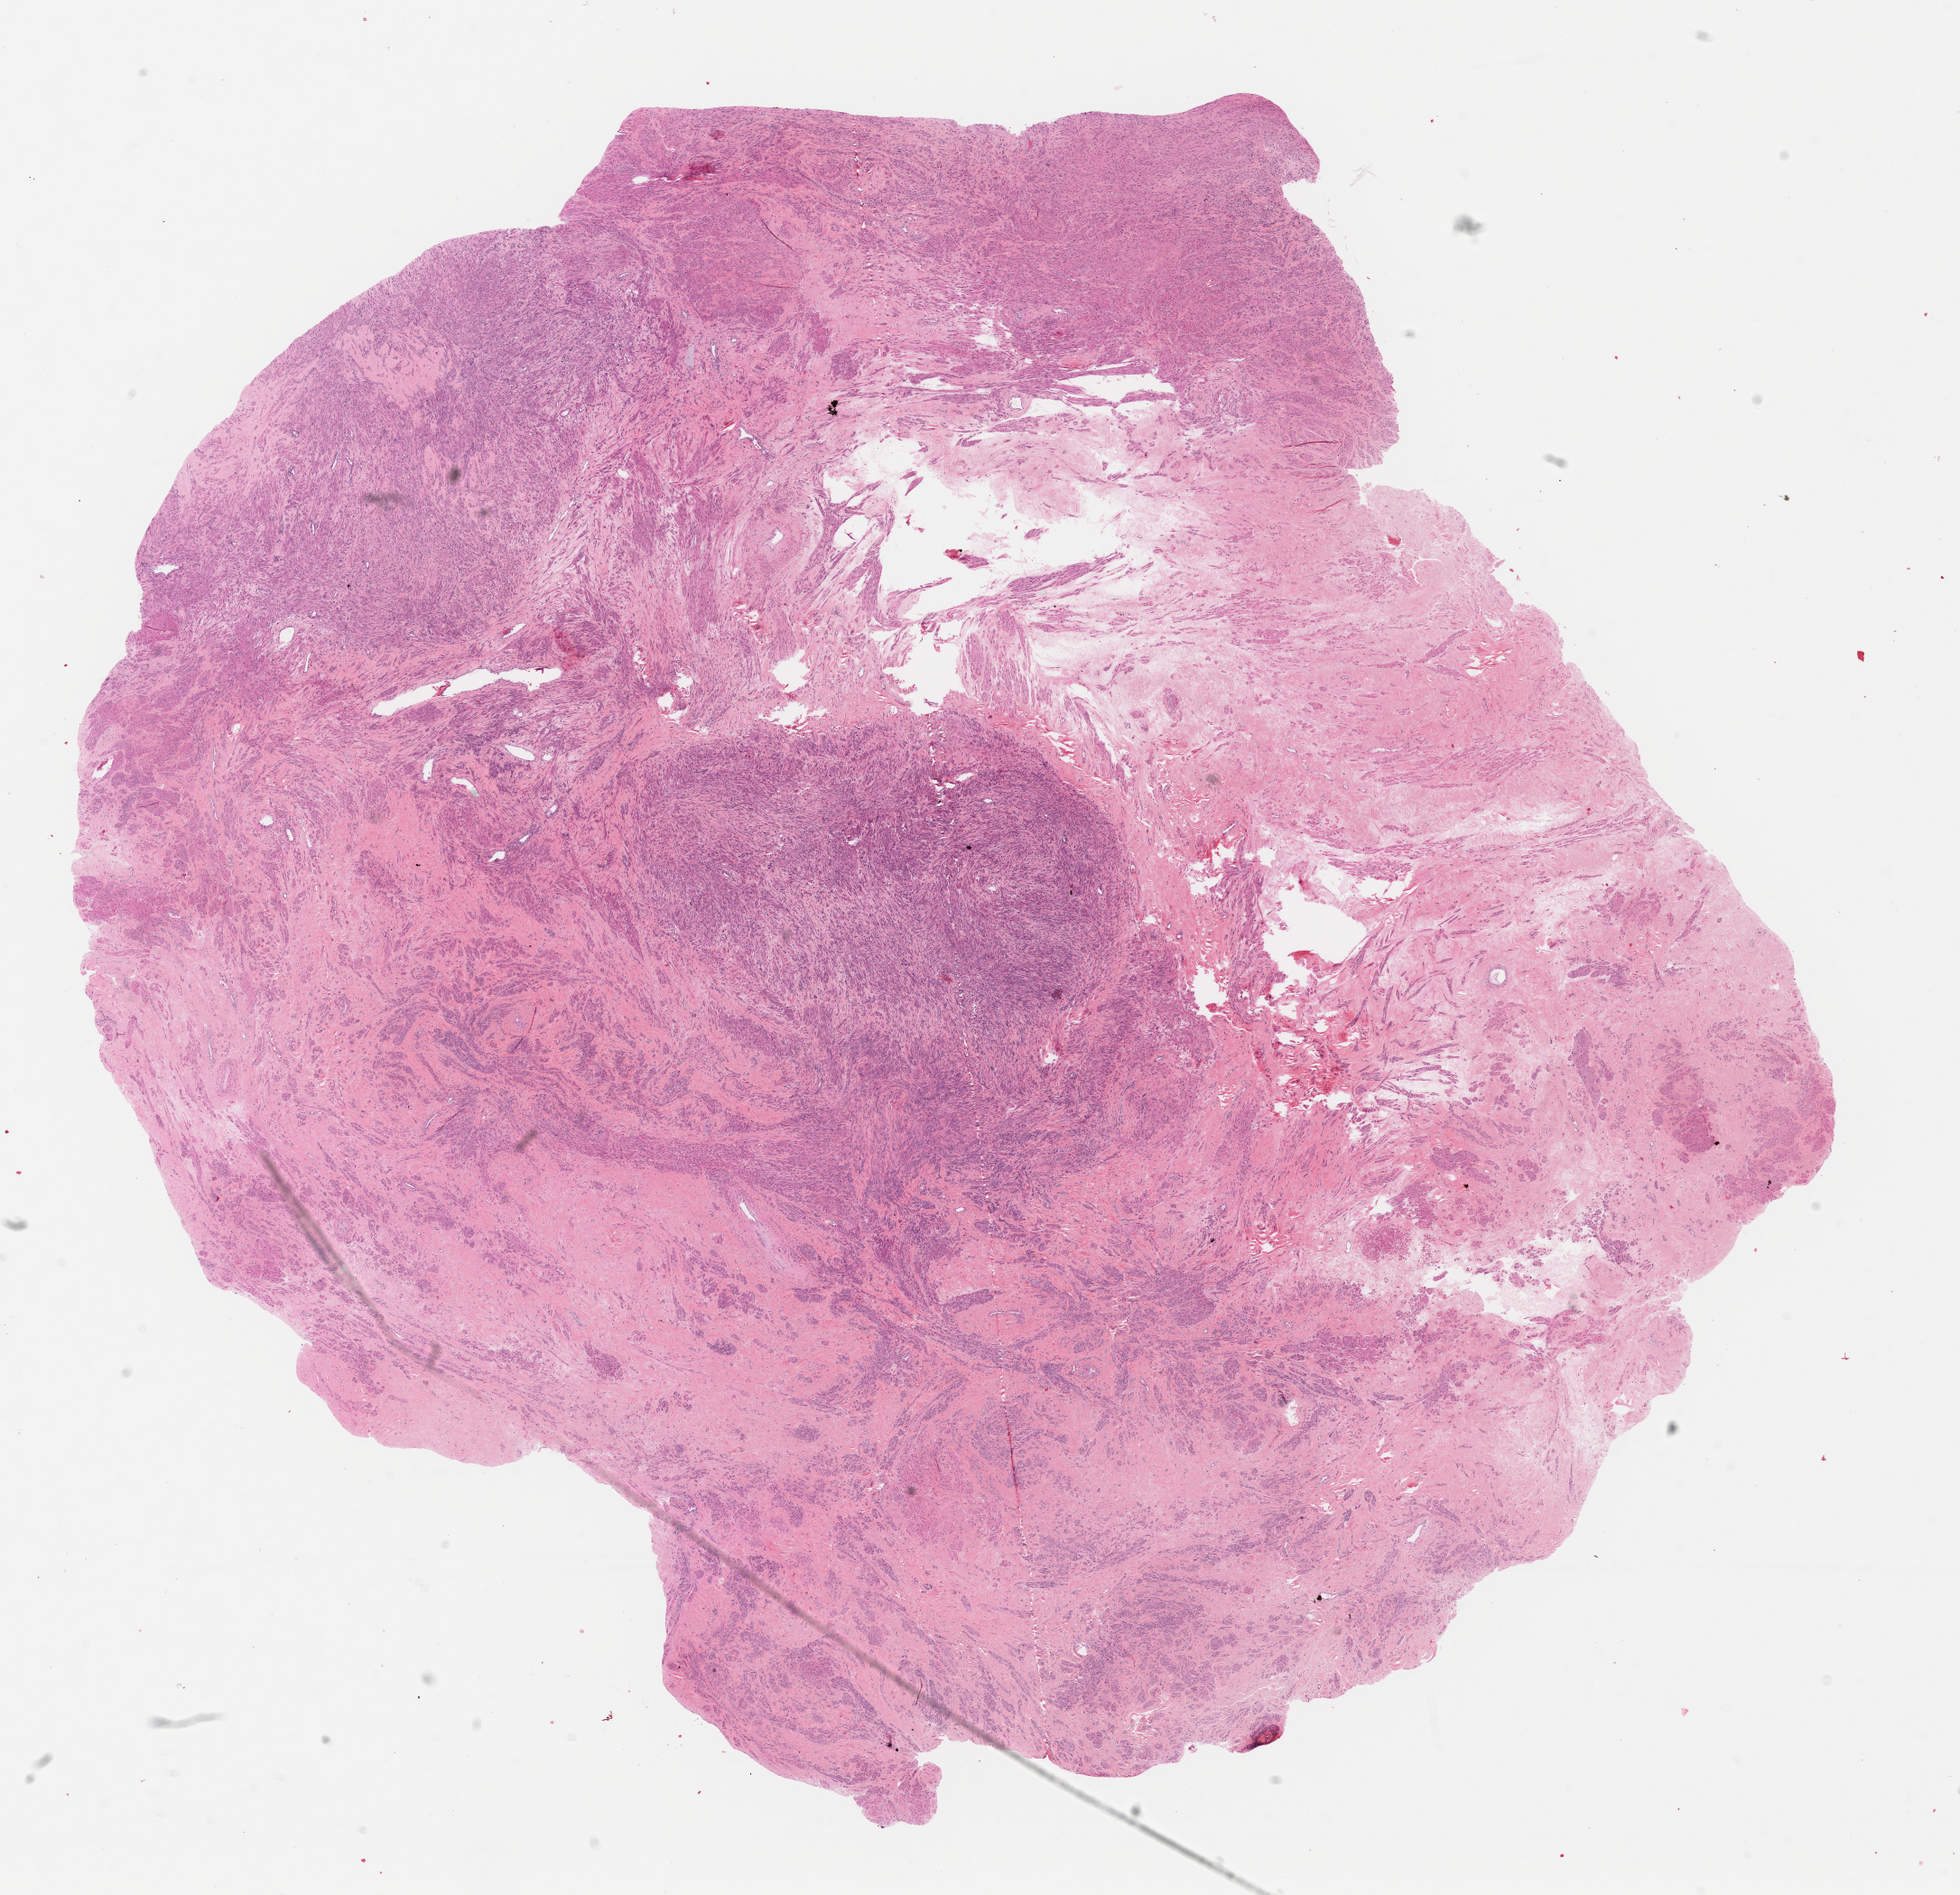
Digitized H&E-stained tissue section (whole slide), low-resolution overview of the scanned area, about 17.1 x 16.6 mm. Formalin-fixed paraffin-embedded (FFPE) diagnostic section. Uterus, primary tumour sample. Female, age 69 years at initial diagnosis.
- diagnosis: Leiomyosarcoma, NOS